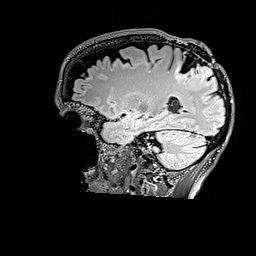
Brain MRI from a brain-tumour surgery series, one sagittal slice; position 116 of 176 along the scan axis; T2 FLAIR; 1 mm slice thickness; 256 × 256 image matrix. From the clinical record (not read from this slice): histopathology: Astrocytoma; WHO grade: 3; IDH mutation: yes; tumour location: Right Parietal.
Outlined on this slice (expert manual segmentation):
- tumour: bounding box (x1, y1, x2, y2) in pixels: (175, 64, 212, 81)
- tumour: (196, 64, 213, 81)